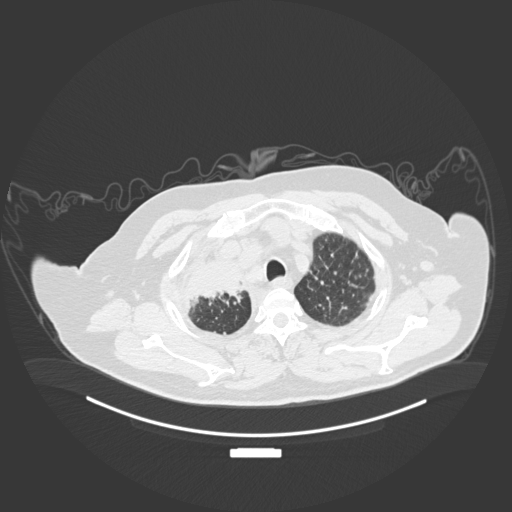
Chest CT, one axial slice; slice 161 of 201 in the series (ordered by position); reconstruction kernel B30f; 120 kVp; lung window (W 1500 / L -600 HU); 1 mm slice thickness; 512 × 512 image matrix, field of view 500 × 500 mm. Male patient, age 69 years. Case-level facts recorded for this patient, not image findings: clinical TNM (as recorded): T4 N3 M1.
Annotated regions visible in this slice (rectangle marked by the reading radiologist):
- lung tumour (recorded histology: adenocarcinoma): bounding box <169,248,254,310> (left, top, right, bottom; pixels)